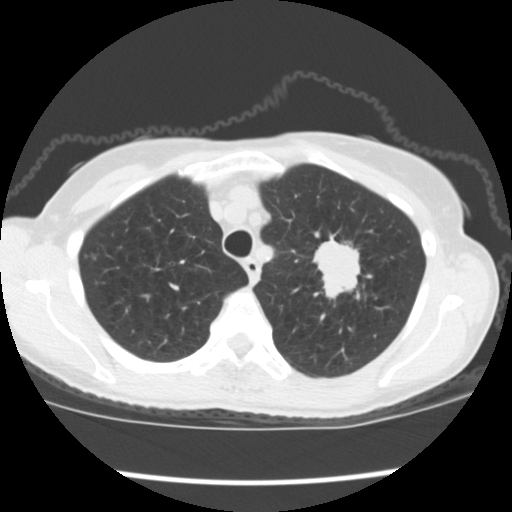
Low-dose screening chest CT, one axial slice. Position 145 of 176 along the scan axis. Reconstruction kernel STANDARD. Lung window (W 1500 / L -600 HU). 2.5 mm slice thickness. 512 × 512 image matrix.
Outlined on this slice (manually delineated by an expert):
- lesion 1 (tumor, upper lobe of left lung): bounding box <313,237,360,299> (left, top, right, bottom; pixels)